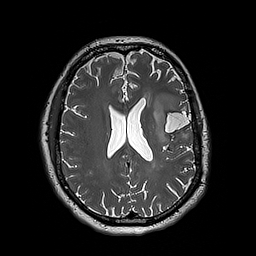
Brain MRI from a brain-tumour surgery series, one axial slice; slice 85 of 192 in the series (ordered by position); 256 × 256 image matrix. Case-level facts recorded for this patient, not image findings: histopathology: Astrocytoma; WHO grade: 3; IDH mutation: yes; tumour location: Left Insular.
Outlined on this slice (outlined manually by an expert reader):
- tumour: box from (x=153, y=93) to (x=180, y=144) px